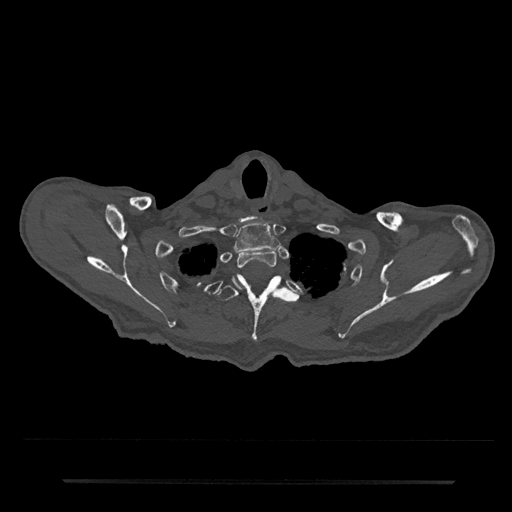
CT including the spine, one axial slice. Slice 684 of 797 in the series (ordered by position). Reconstruction kernel Br40s/3. 120 kVp. Bone window (W 1800 / L 400 HU). 0.5 mm slice thickness. 512 × 512 image matrix. Patient: male, 74 years. From the clinical record (not read from this slice): primary cancer: prostate.
Annotated regions visible in this slice (semi-automatic segmentation, software-assisted and operator-edited):
- T1 vertebra: box from (x=233, y=222) to (x=281, y=253) px
- T2 vertebra: (x=232, y=250)–(x=277, y=289)
- T3 vertebra: (x=216, y=274)–(x=298, y=342)